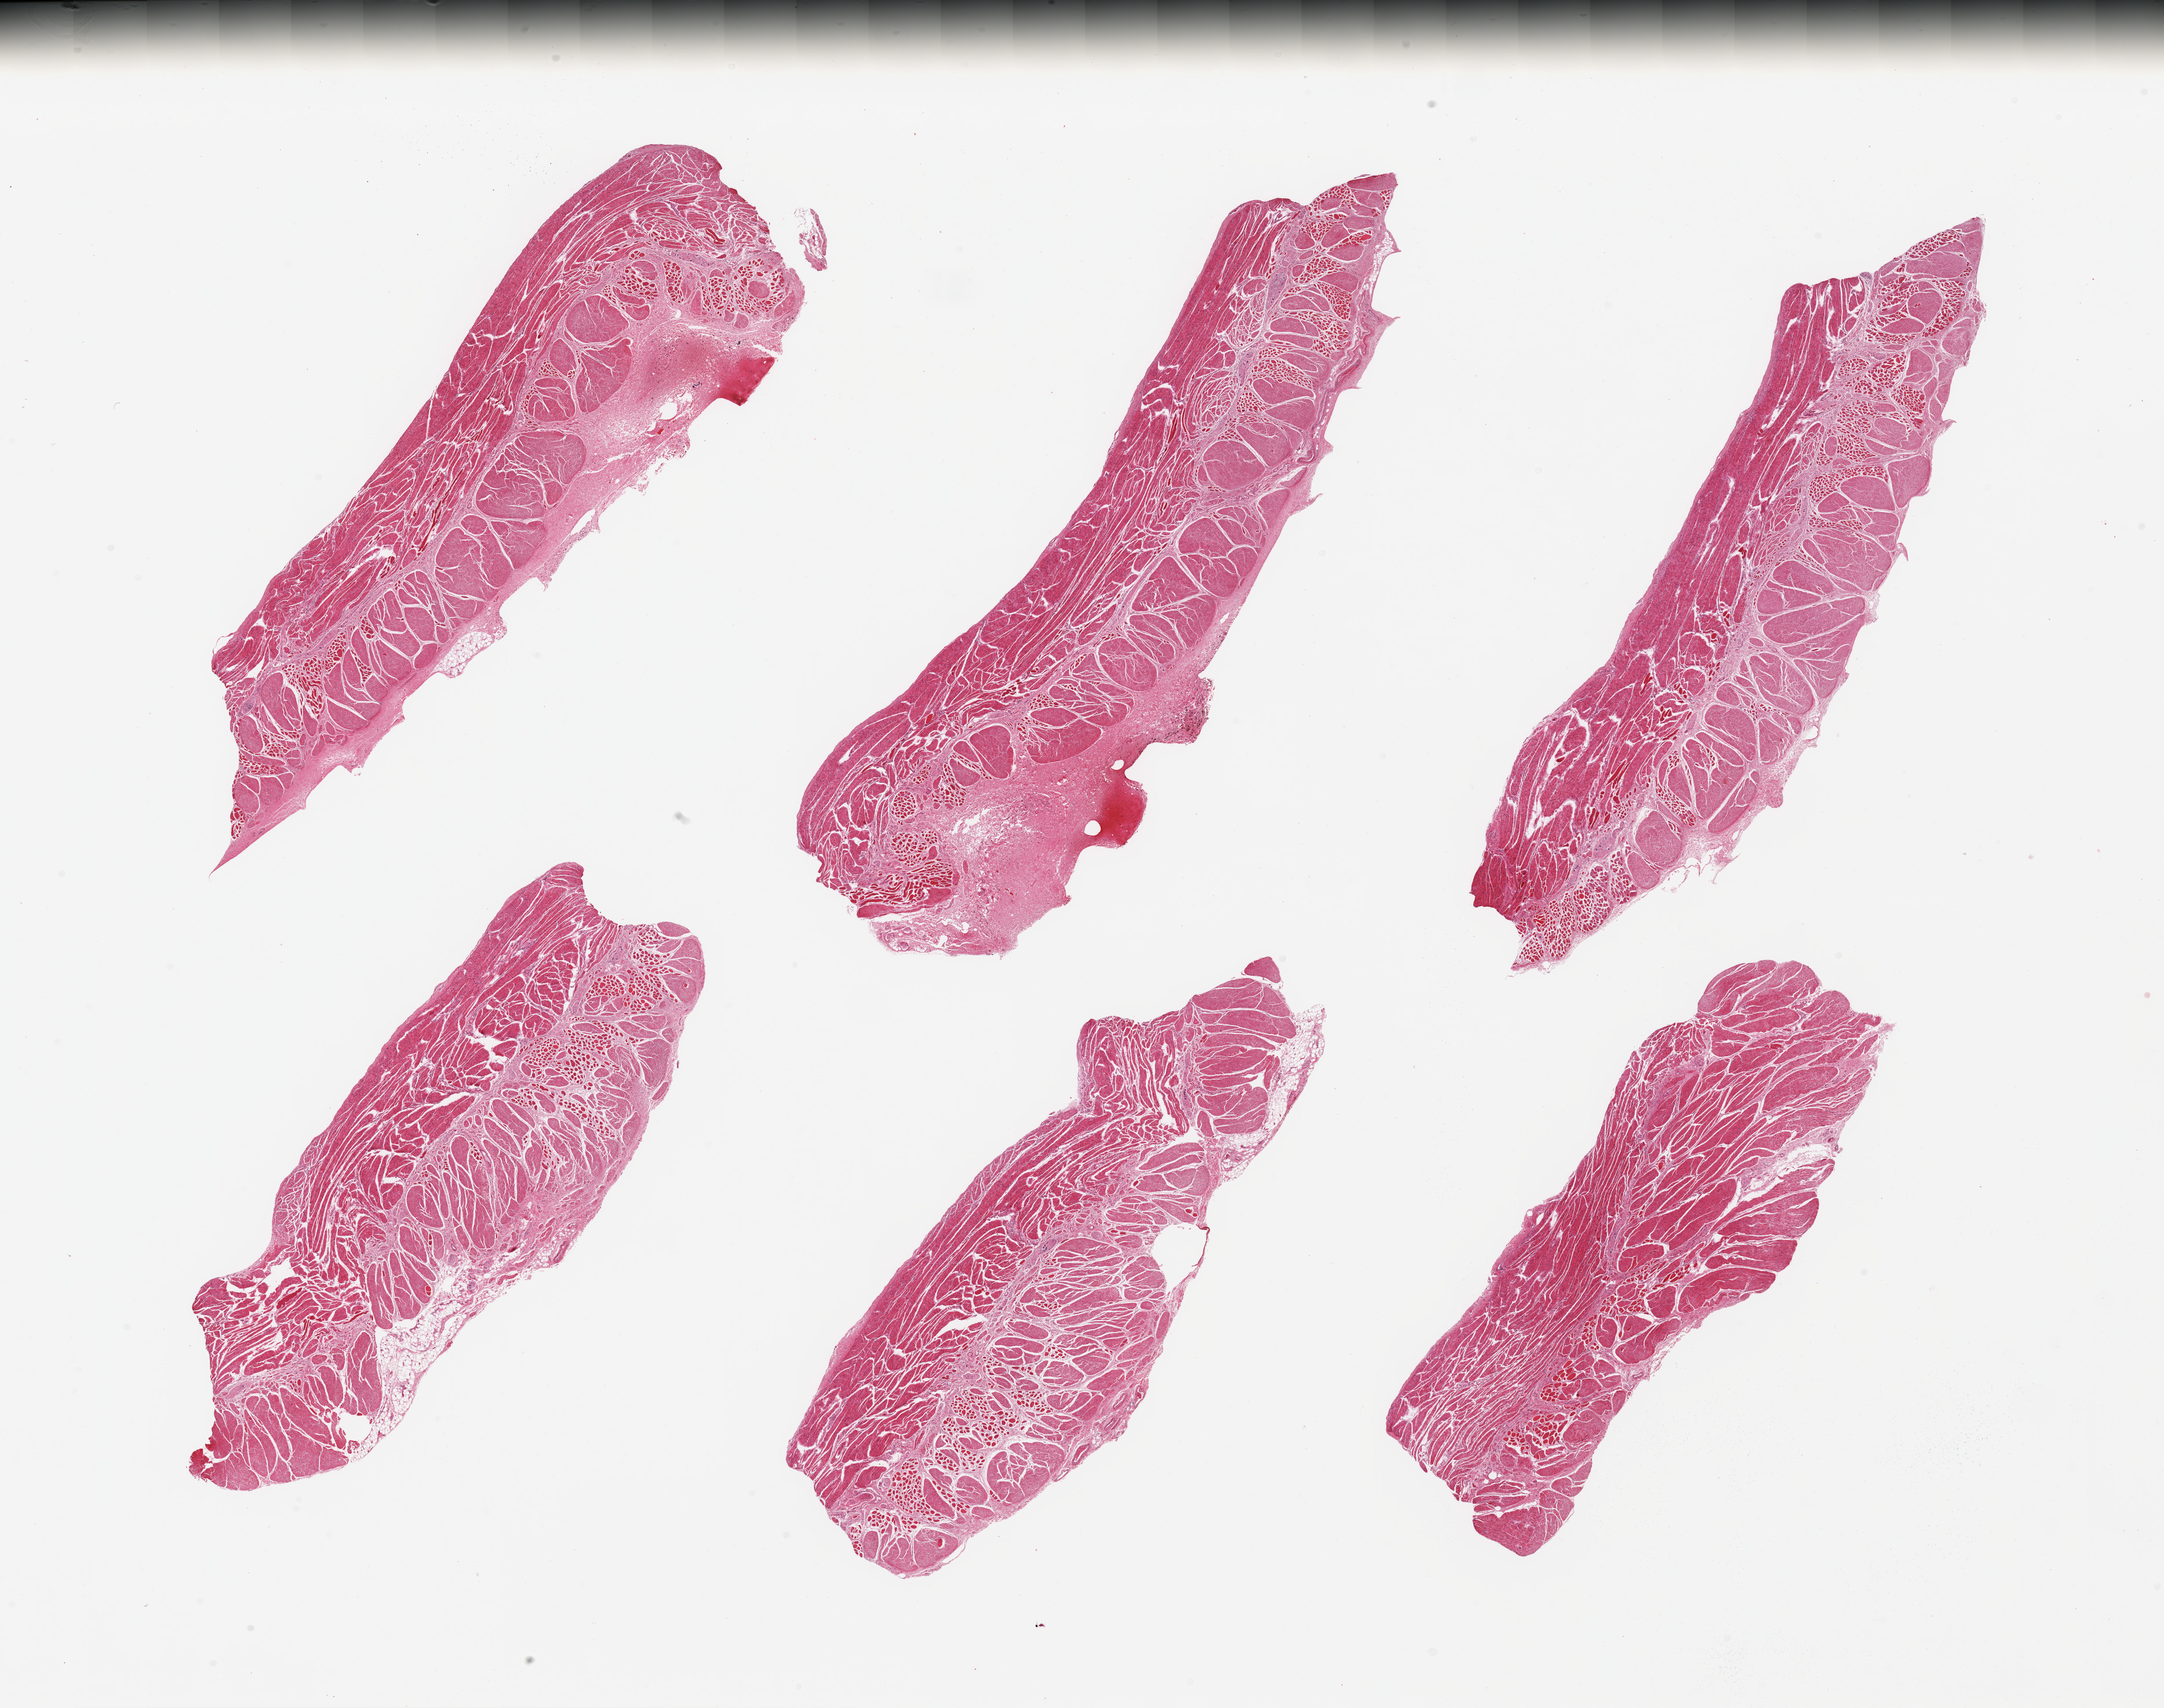
Whole-slide image, H&E stain, brightfield, shown as a low-resolution overview of the whole scanned area (about 29.5 x 23.3 mm, from a 20x scan). PAXgene-fixed, paraffin-embedded tissue. Section of esophageal muscle (target tissue). Tissue donor sample. Donor: male.
Reviewer comment on this tissue sample: 6 pieces; target muscularis and small amounts of attached serosa, focally hemorrhagic with hemosiderinophages.